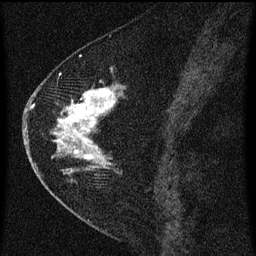
Breast MRI (dynamic contrast-enhanced), one sagittal slice; slice 30 of 60 in the series (ordered by position); dynamic contrast-enhanced series, image 2 of 3 at this slice position (ordered by acquisition); 1.5 T; TE 4.2 ms, TR 8 ms; 2 mm slice thickness; 256 × 256 image matrix, field of view 180 × 180 mm. Female patient, age 47 years.
Outlined on this slice (semi-automatically segmented with operator editing):
- analysis volume of interest (the breast-tissue region the enhancement analysis was run in; not a lesion): box from (x=38, y=76) to (x=125, y=193) px
- tumour enhancement mask (voxels above the 70 % enhancement threshold inside the analysis volume of interest): (x=54, y=86)–(x=122, y=173)